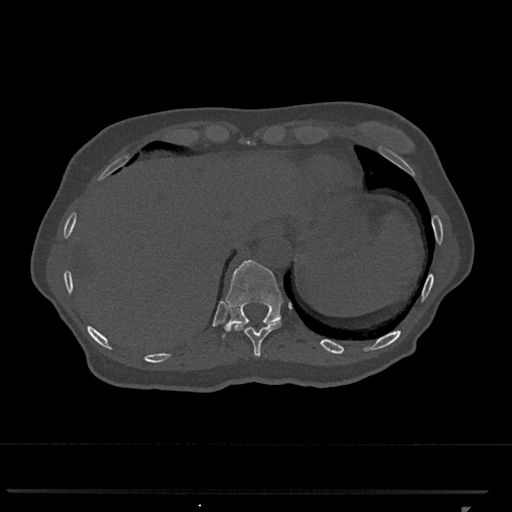
CT including the spine, one axial slice. Position 542 of 793 along the scan axis. 120 kVp. Bone window (W 1800 / L 400 HU). 0.5 mm slice thickness. 512 × 512 image matrix. Patient: female, 62 years. From the clinical record (not read from this slice): primary cancer: renal.
Outlined on this slice (semi-automatic segmentation, software-assisted and operator-edited):
- T10 vertebra: bounding box [x1, y1, x2, y2] px = [230, 322, 281, 357]
- T11 vertebra: [222, 260, 283, 338]